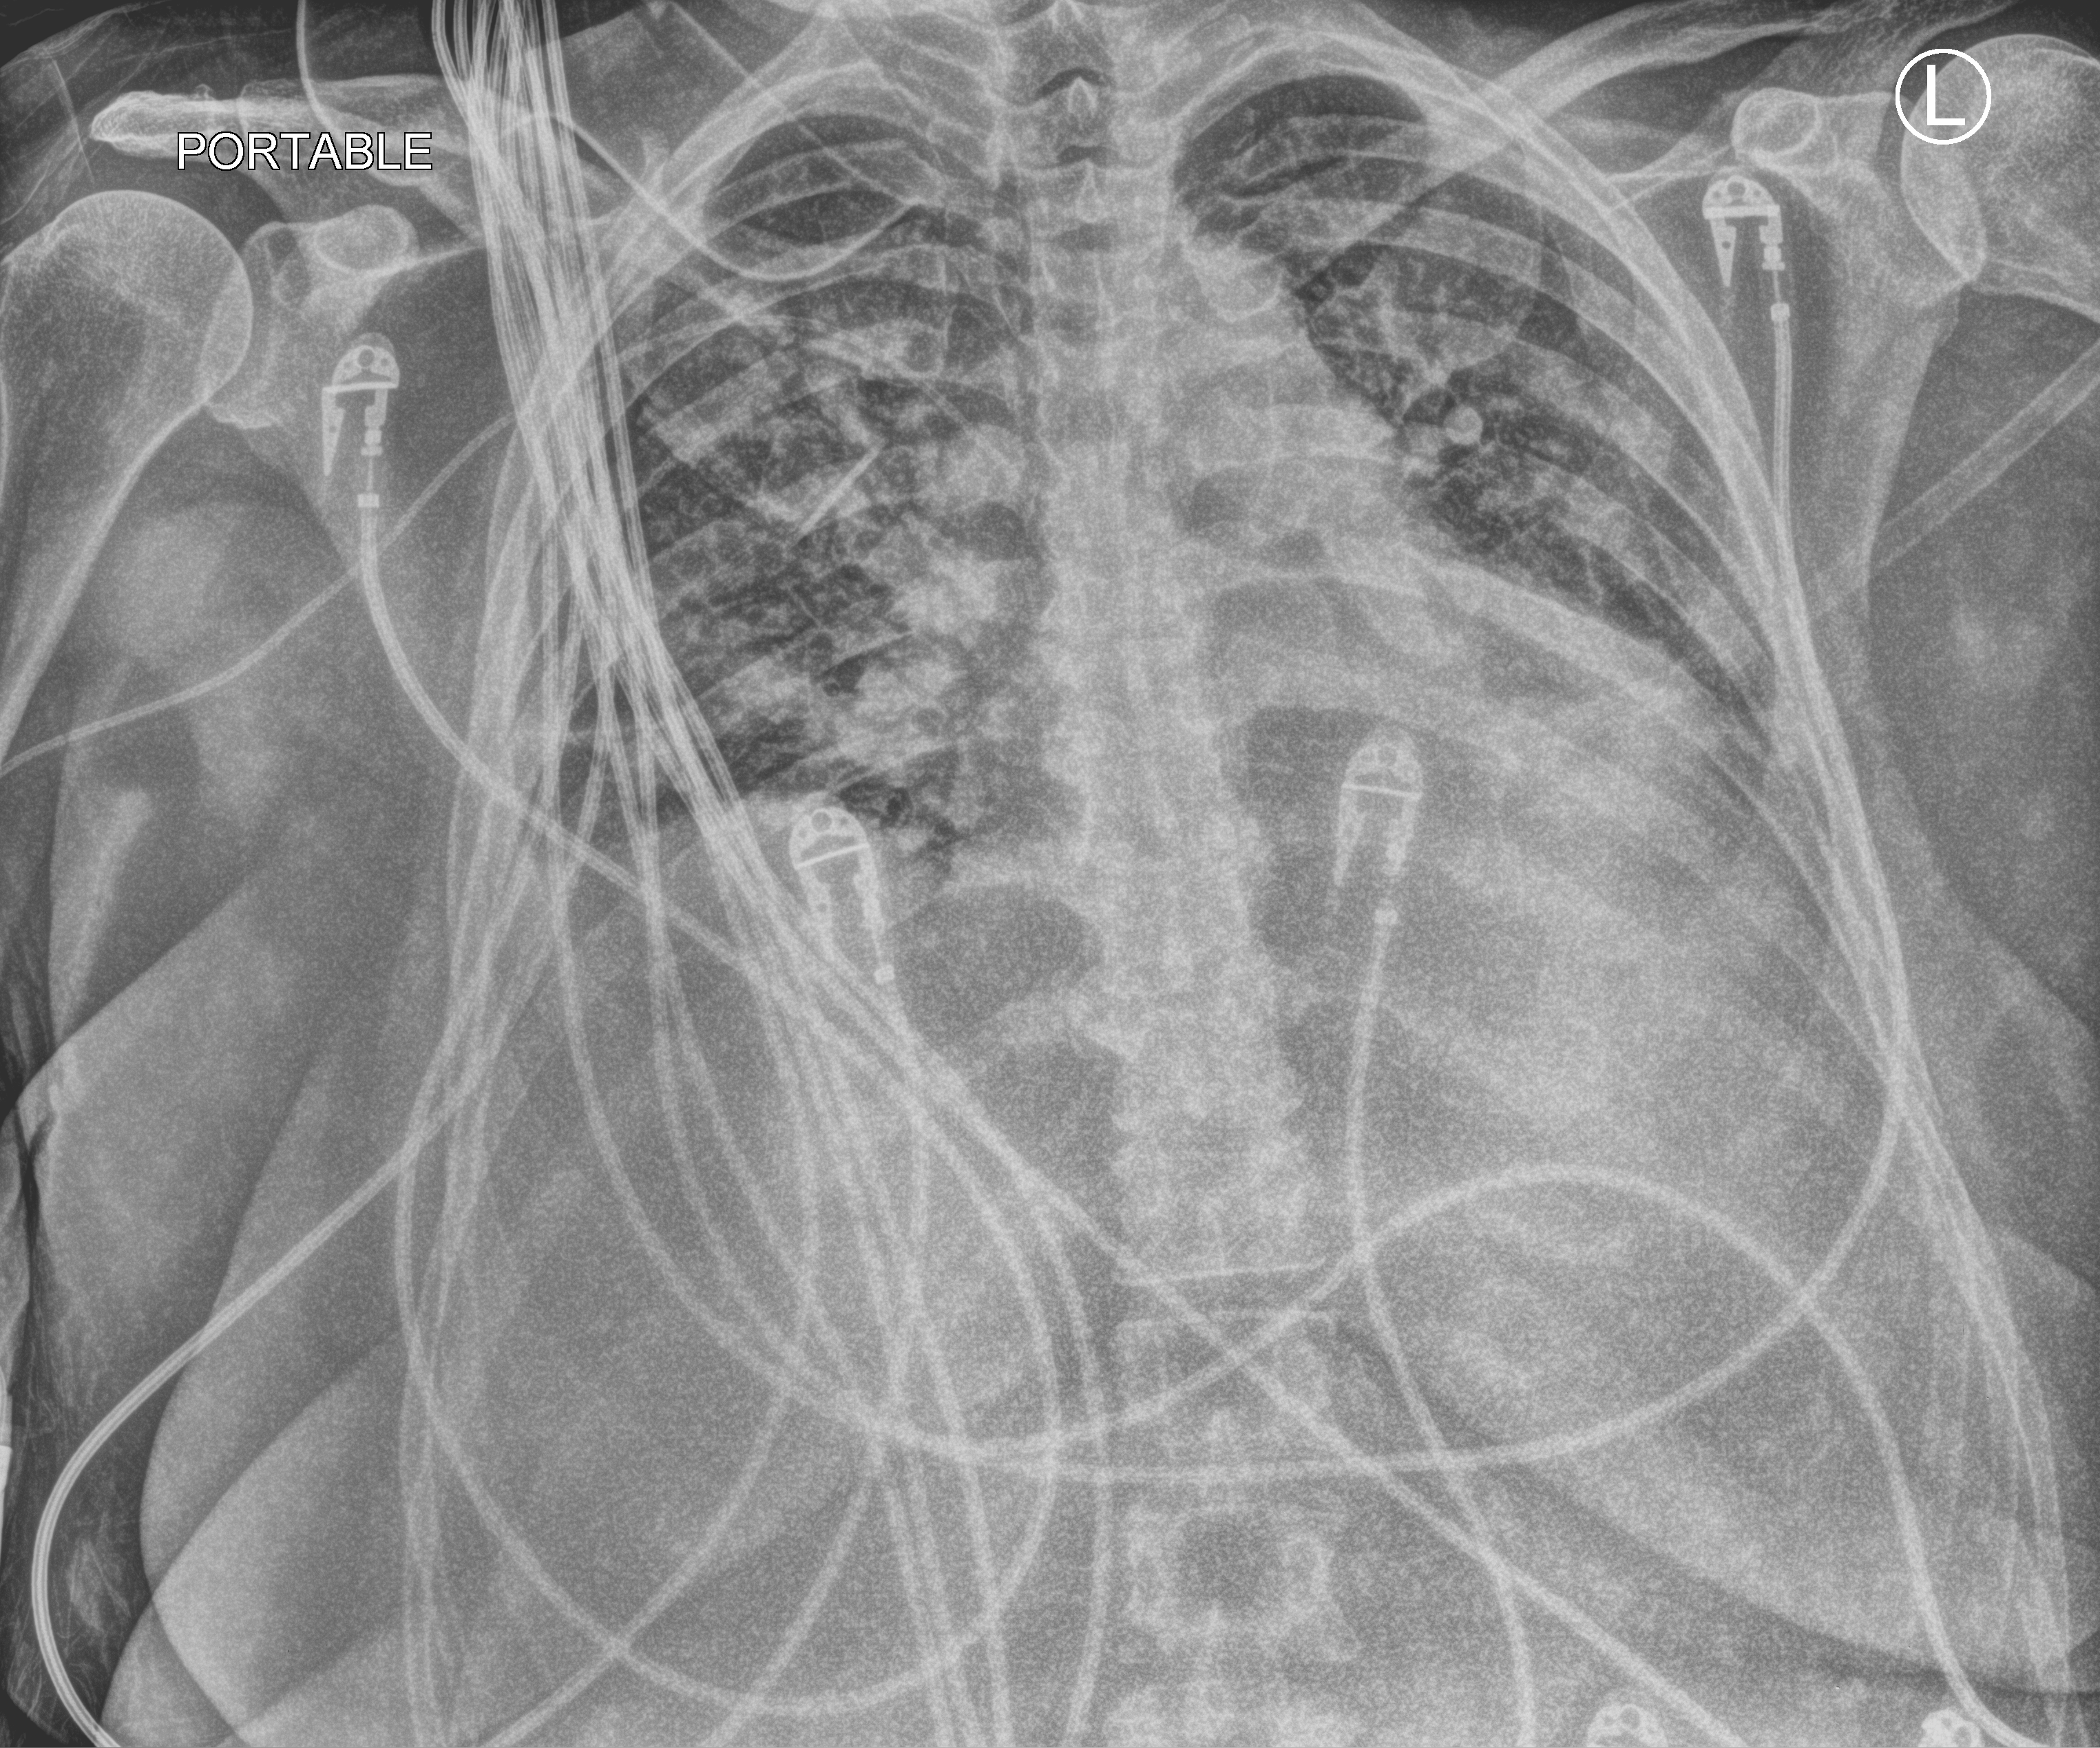
Portable chest radiograph; anteroposterior (AP) projection. Patient hospitalised with COVID-19; female, aged 60–74 years.
Hospital-stay facts (about this admission, not read from this image; timing relative to this image not recorded):
- length of hospital stay: 50 days
- mechanically ventilated during this hospital stay: yes